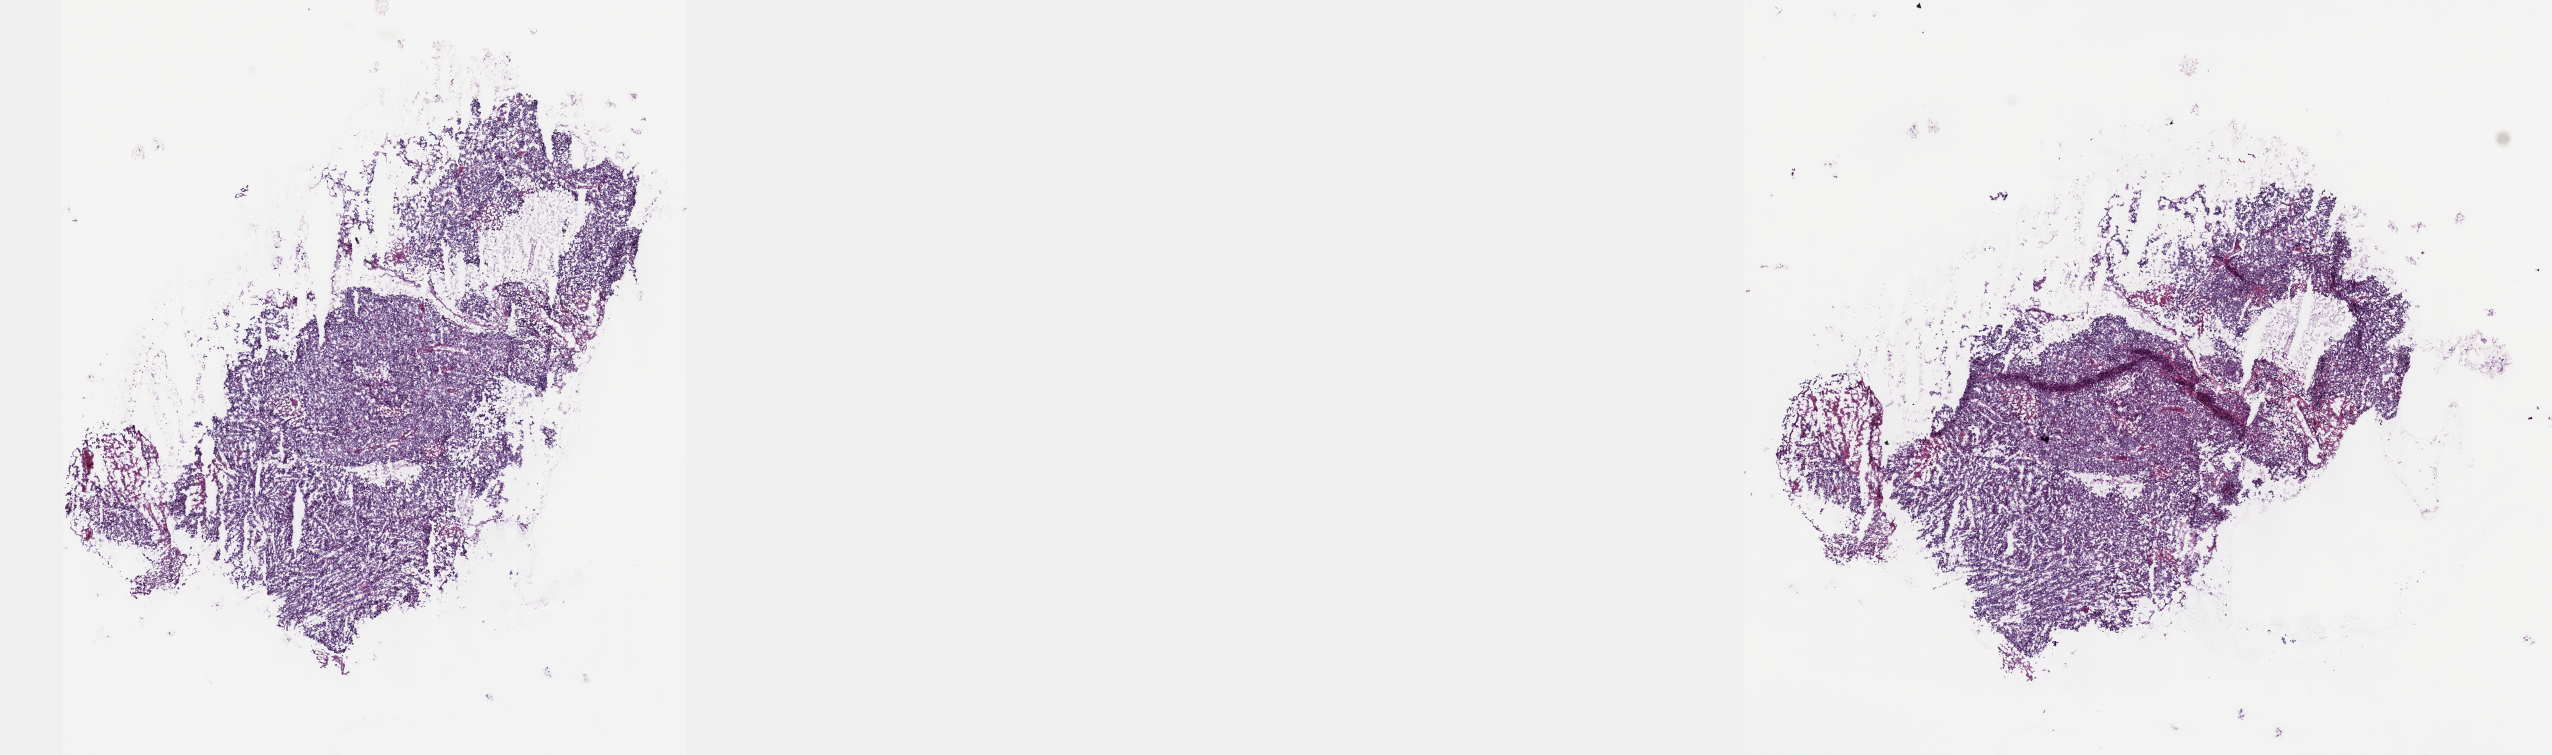
Whole-slide histology image, Hematoxylin and eosin (H&E) stained, whole scanned area (about 20.6 x 6.1 mm, from a 40x scan) shown as a low-resolution overview. Frozen section from the top of the tissue portion. Primary tumour sample from the cervix. Female, age 79 years at initial diagnosis. Histologic grade: G3 (poorly differentiated). Slide review estimates, as recorded: tumour cells 80%, tumour nuclei 80%, normal cells 0%, stromal cells 15%, necrosis 5%. Infiltration values recorded for this section: lymphocyte infiltration 5%, monocyte infiltration 0%, neutrophil infiltration 5%.
Diagnosis: Squamous cell carcinoma, NOS (cervix uteri). FIGO stage: IIIB.